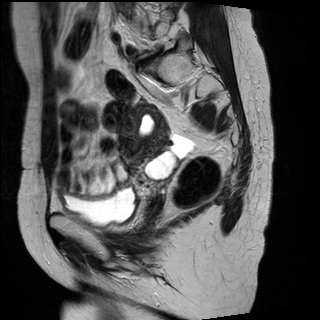
Pelvic MRI for cervical cancer, one sagittal slice; position 11 of 29 along the scan axis; T2-weighted; 1.5 T; TE 89 ms, TR 2930 ms; 320 × 320 image matrix, field of view 260 × 260 mm. Patient: female, 45 years.
Annotated regions visible in this slice (outlined manually by an expert reader):
- uterus and cervix: box from (x=119, y=103) to (x=170, y=170) px